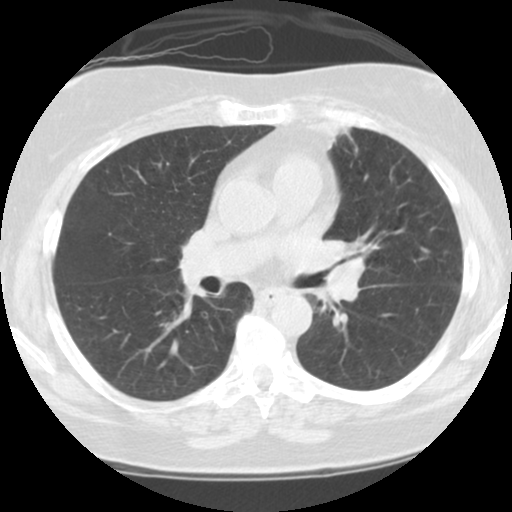
Low-dose screening chest CT, one axial slice; slice 62 of 108 in the series (ordered by position); lung window (W 1500 / L -600 HU); 2.5 mm slice thickness; 512 × 512 image matrix.
Annotated regions visible in this slice (outlined manually by an expert reader):
- lesion 1 (tumor, hilum of left lung): bounding box [x1, y1, x2, y2] px = [315, 239, 365, 303]